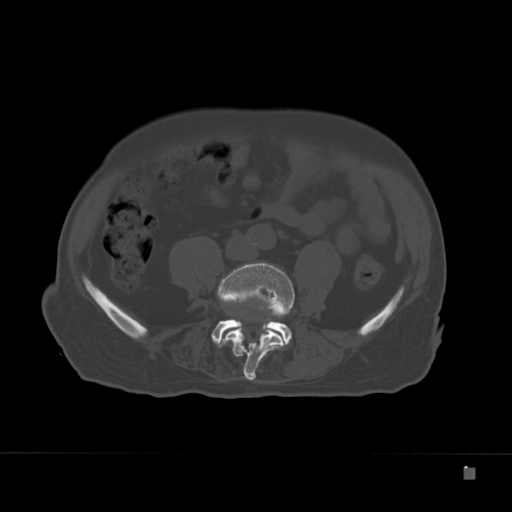
CT including the spine, one axial slice; position 36 of 332 along the scan axis; 120 kVp; bone window (W 1800 / L 400 HU); 1.5 mm slice thickness; 512 × 512 image matrix. Patient: male, 72 years. Case-level facts recorded for this patient, not image findings: primary cancer: skeletal.
Annotated regions visible in this slice (semi-automatically segmented with operator editing):
- L4 vertebra: bounding box (x1, y1, x2, y2) in pixels: (223, 263, 295, 381)
- L5 vertebra: (211, 318, 292, 347)